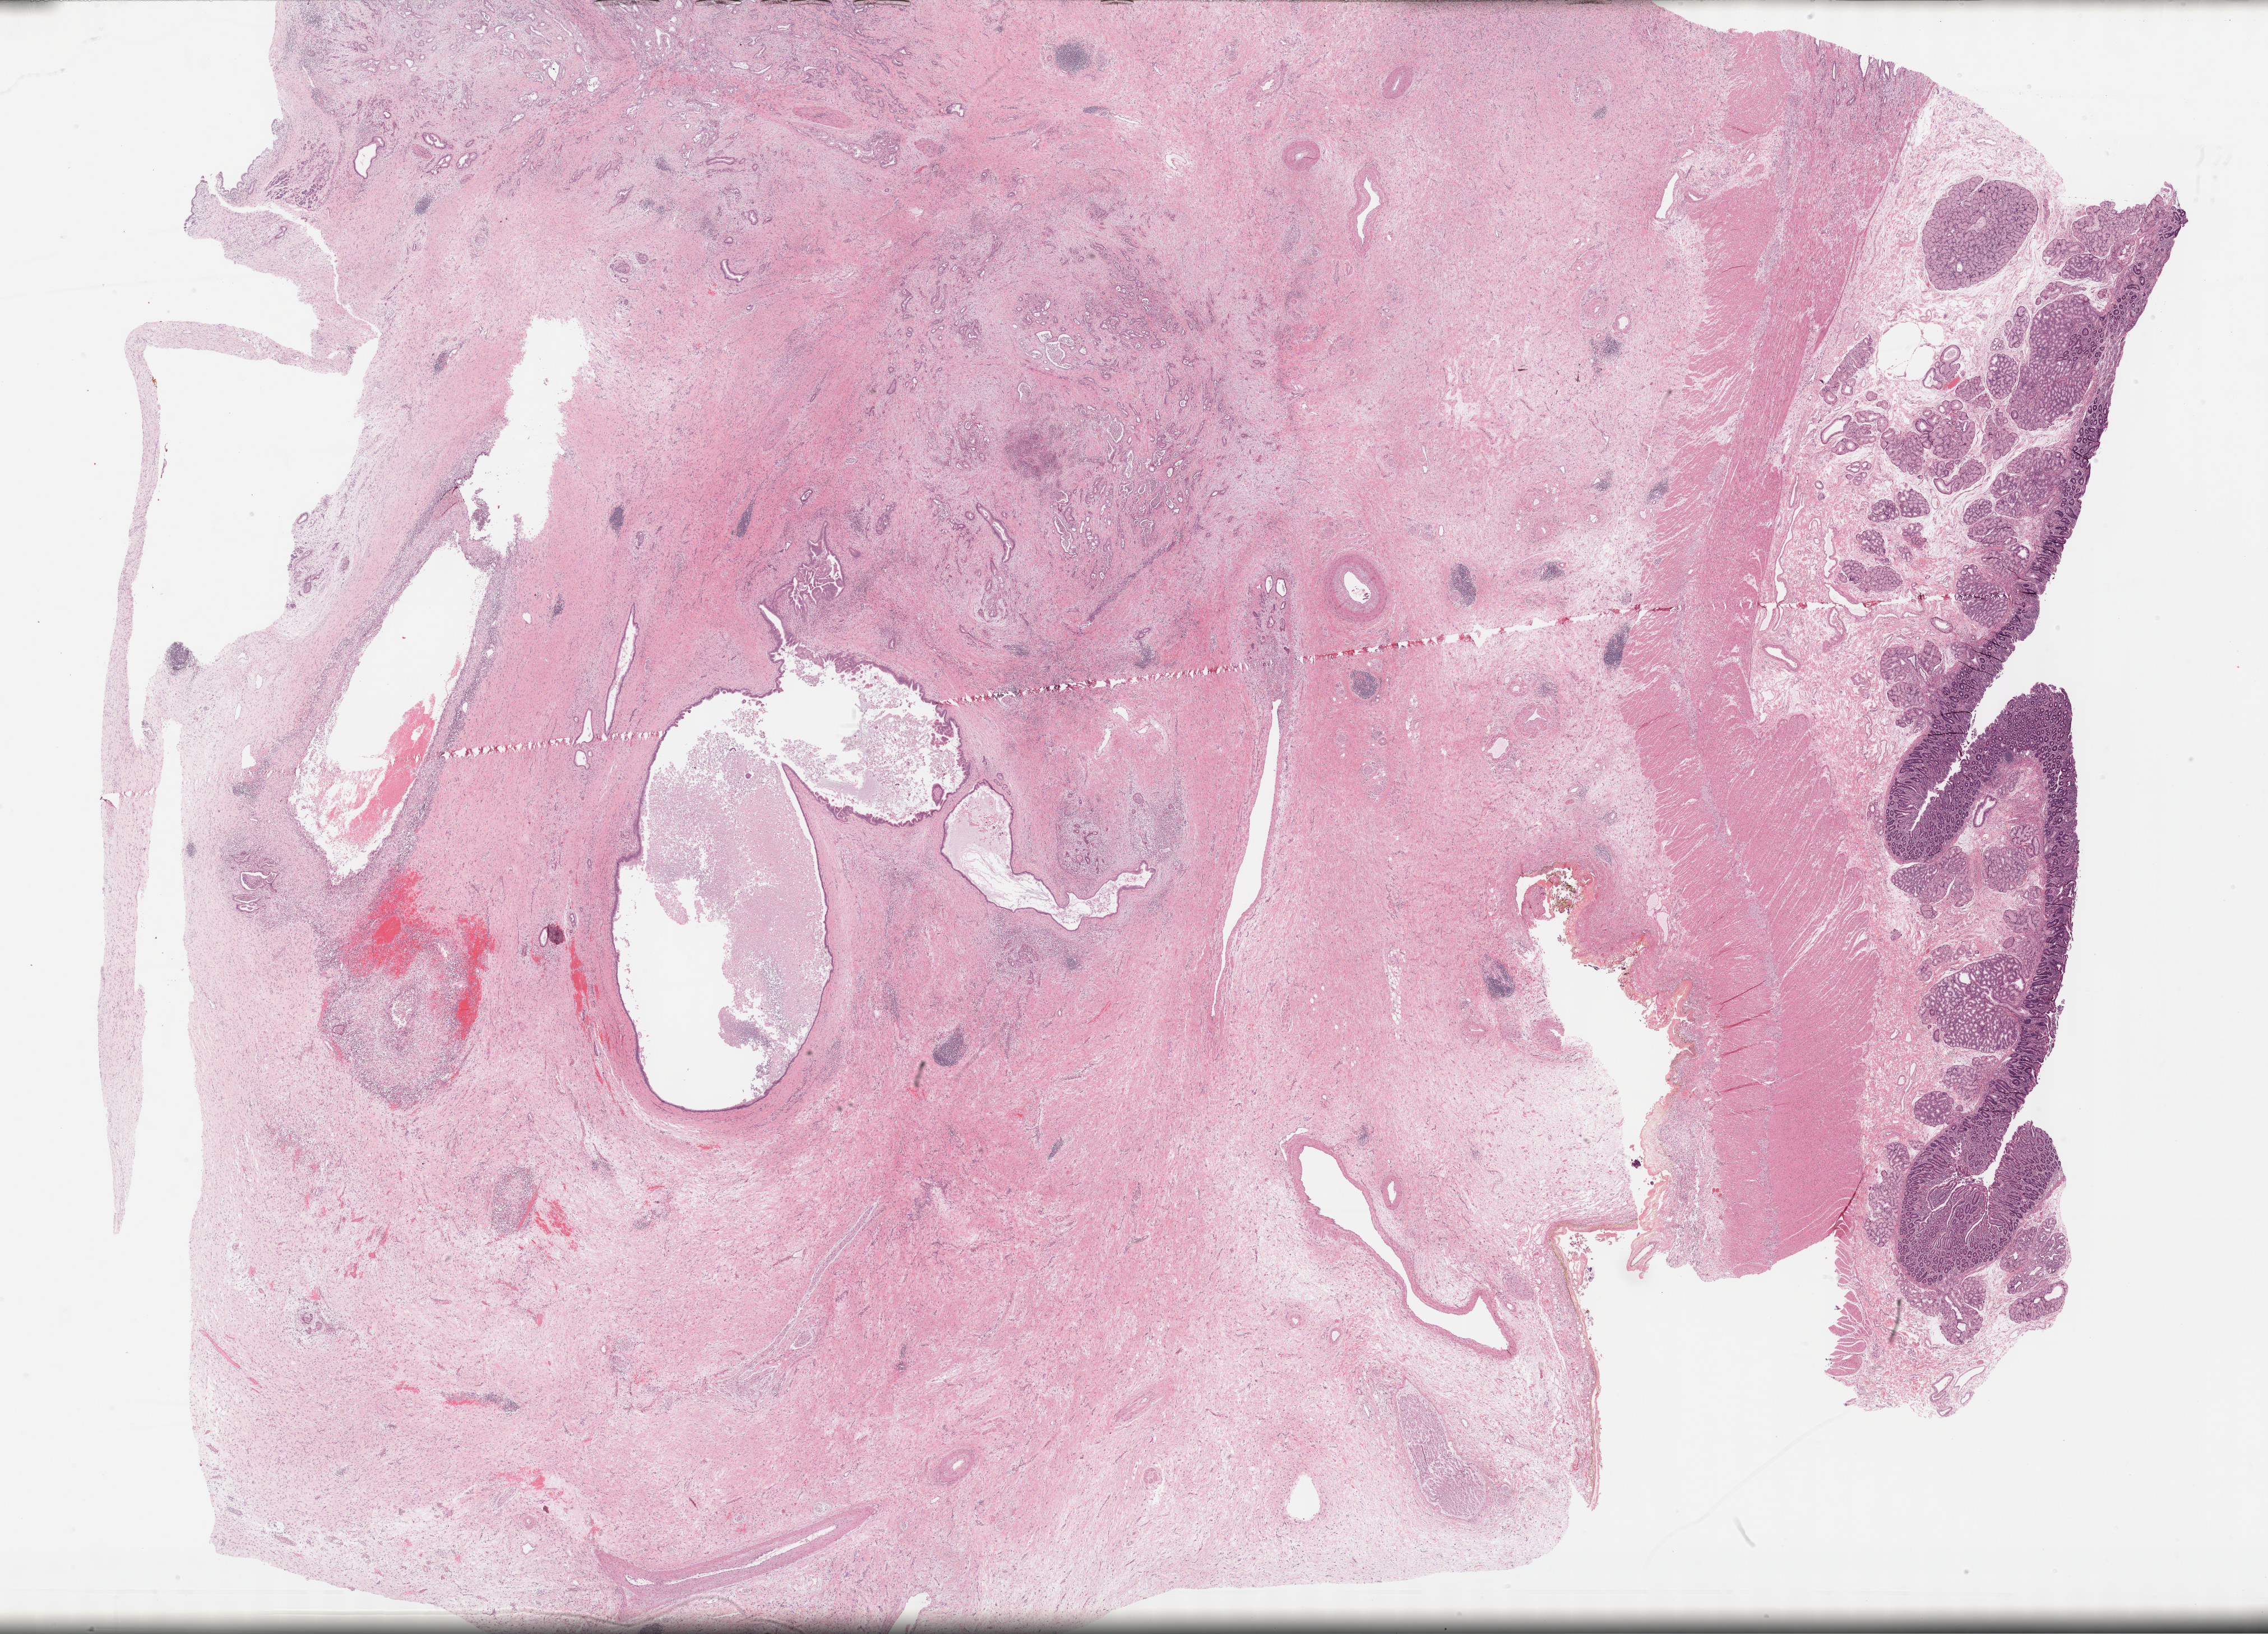
Whole-slide histology image, Hematoxylin and eosin (H&E) stained — a low-resolution overview of the entire scanned area, about 32.7 x 23.6 mm, formalin-fixed paraffin-embedded (FFPE) diagnostic section, sample: primary tumour, pancreas. Patient: female, age at initial diagnosis 62 years. Histologic grade: G2 (moderately differentiated).
AJCC pathologic stage: IIB (7th edition). Lymph nodes positive (case pathology): 3 of 8 examined. TNM: T3 N1 M0. Diagnosis: Infiltrating duct carcinoma, NOS.